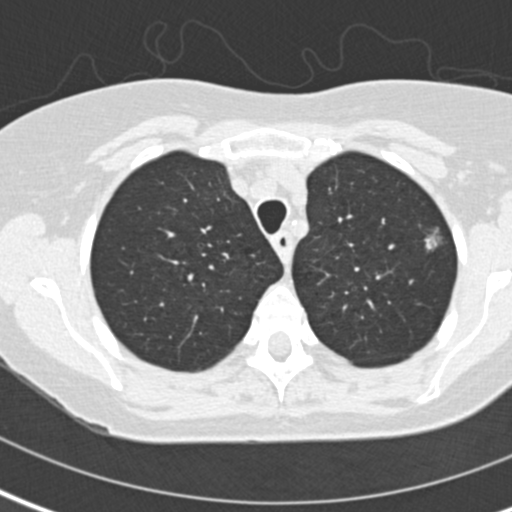
Low-dose screening chest CT, one axial slice; reconstruction kernel B30f; 120 kVp; lung window (W 1500 / L -600 HU); 2 mm slice thickness; 512 × 512 image matrix.
Structures marked on this image (outlined manually by an expert reader):
- lesion 1 (tumor, upper lobe of left lung): box from (x=425, y=227) to (x=441, y=250) px